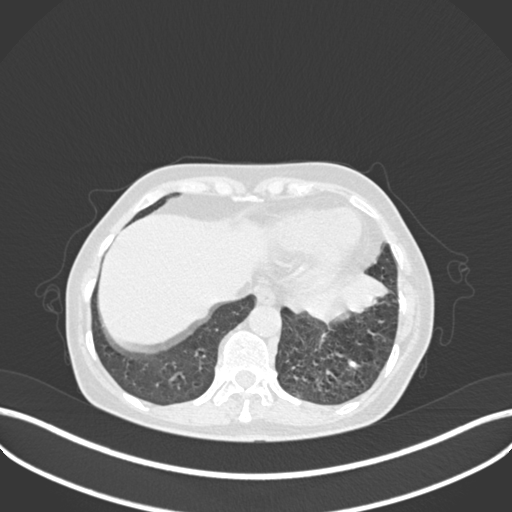
Chest CT, one axial slice; position 53 of 270 along the scan axis; 120 kVp; lung window (W 1500 / L -600 HU); 1 mm slice thickness; 512 × 512 image matrix, field of view 400 × 400 mm. Patient: female, 63 years. Case-level facts recorded for this patient, not image findings: clinical TNM (as recorded): T1b N0 M0.
Annotated regions visible in this slice (rectangle marked by the reading radiologist):
- lung tumour (recorded histology: adenocarcinoma): box from (x=283, y=267) to (x=391, y=329) px